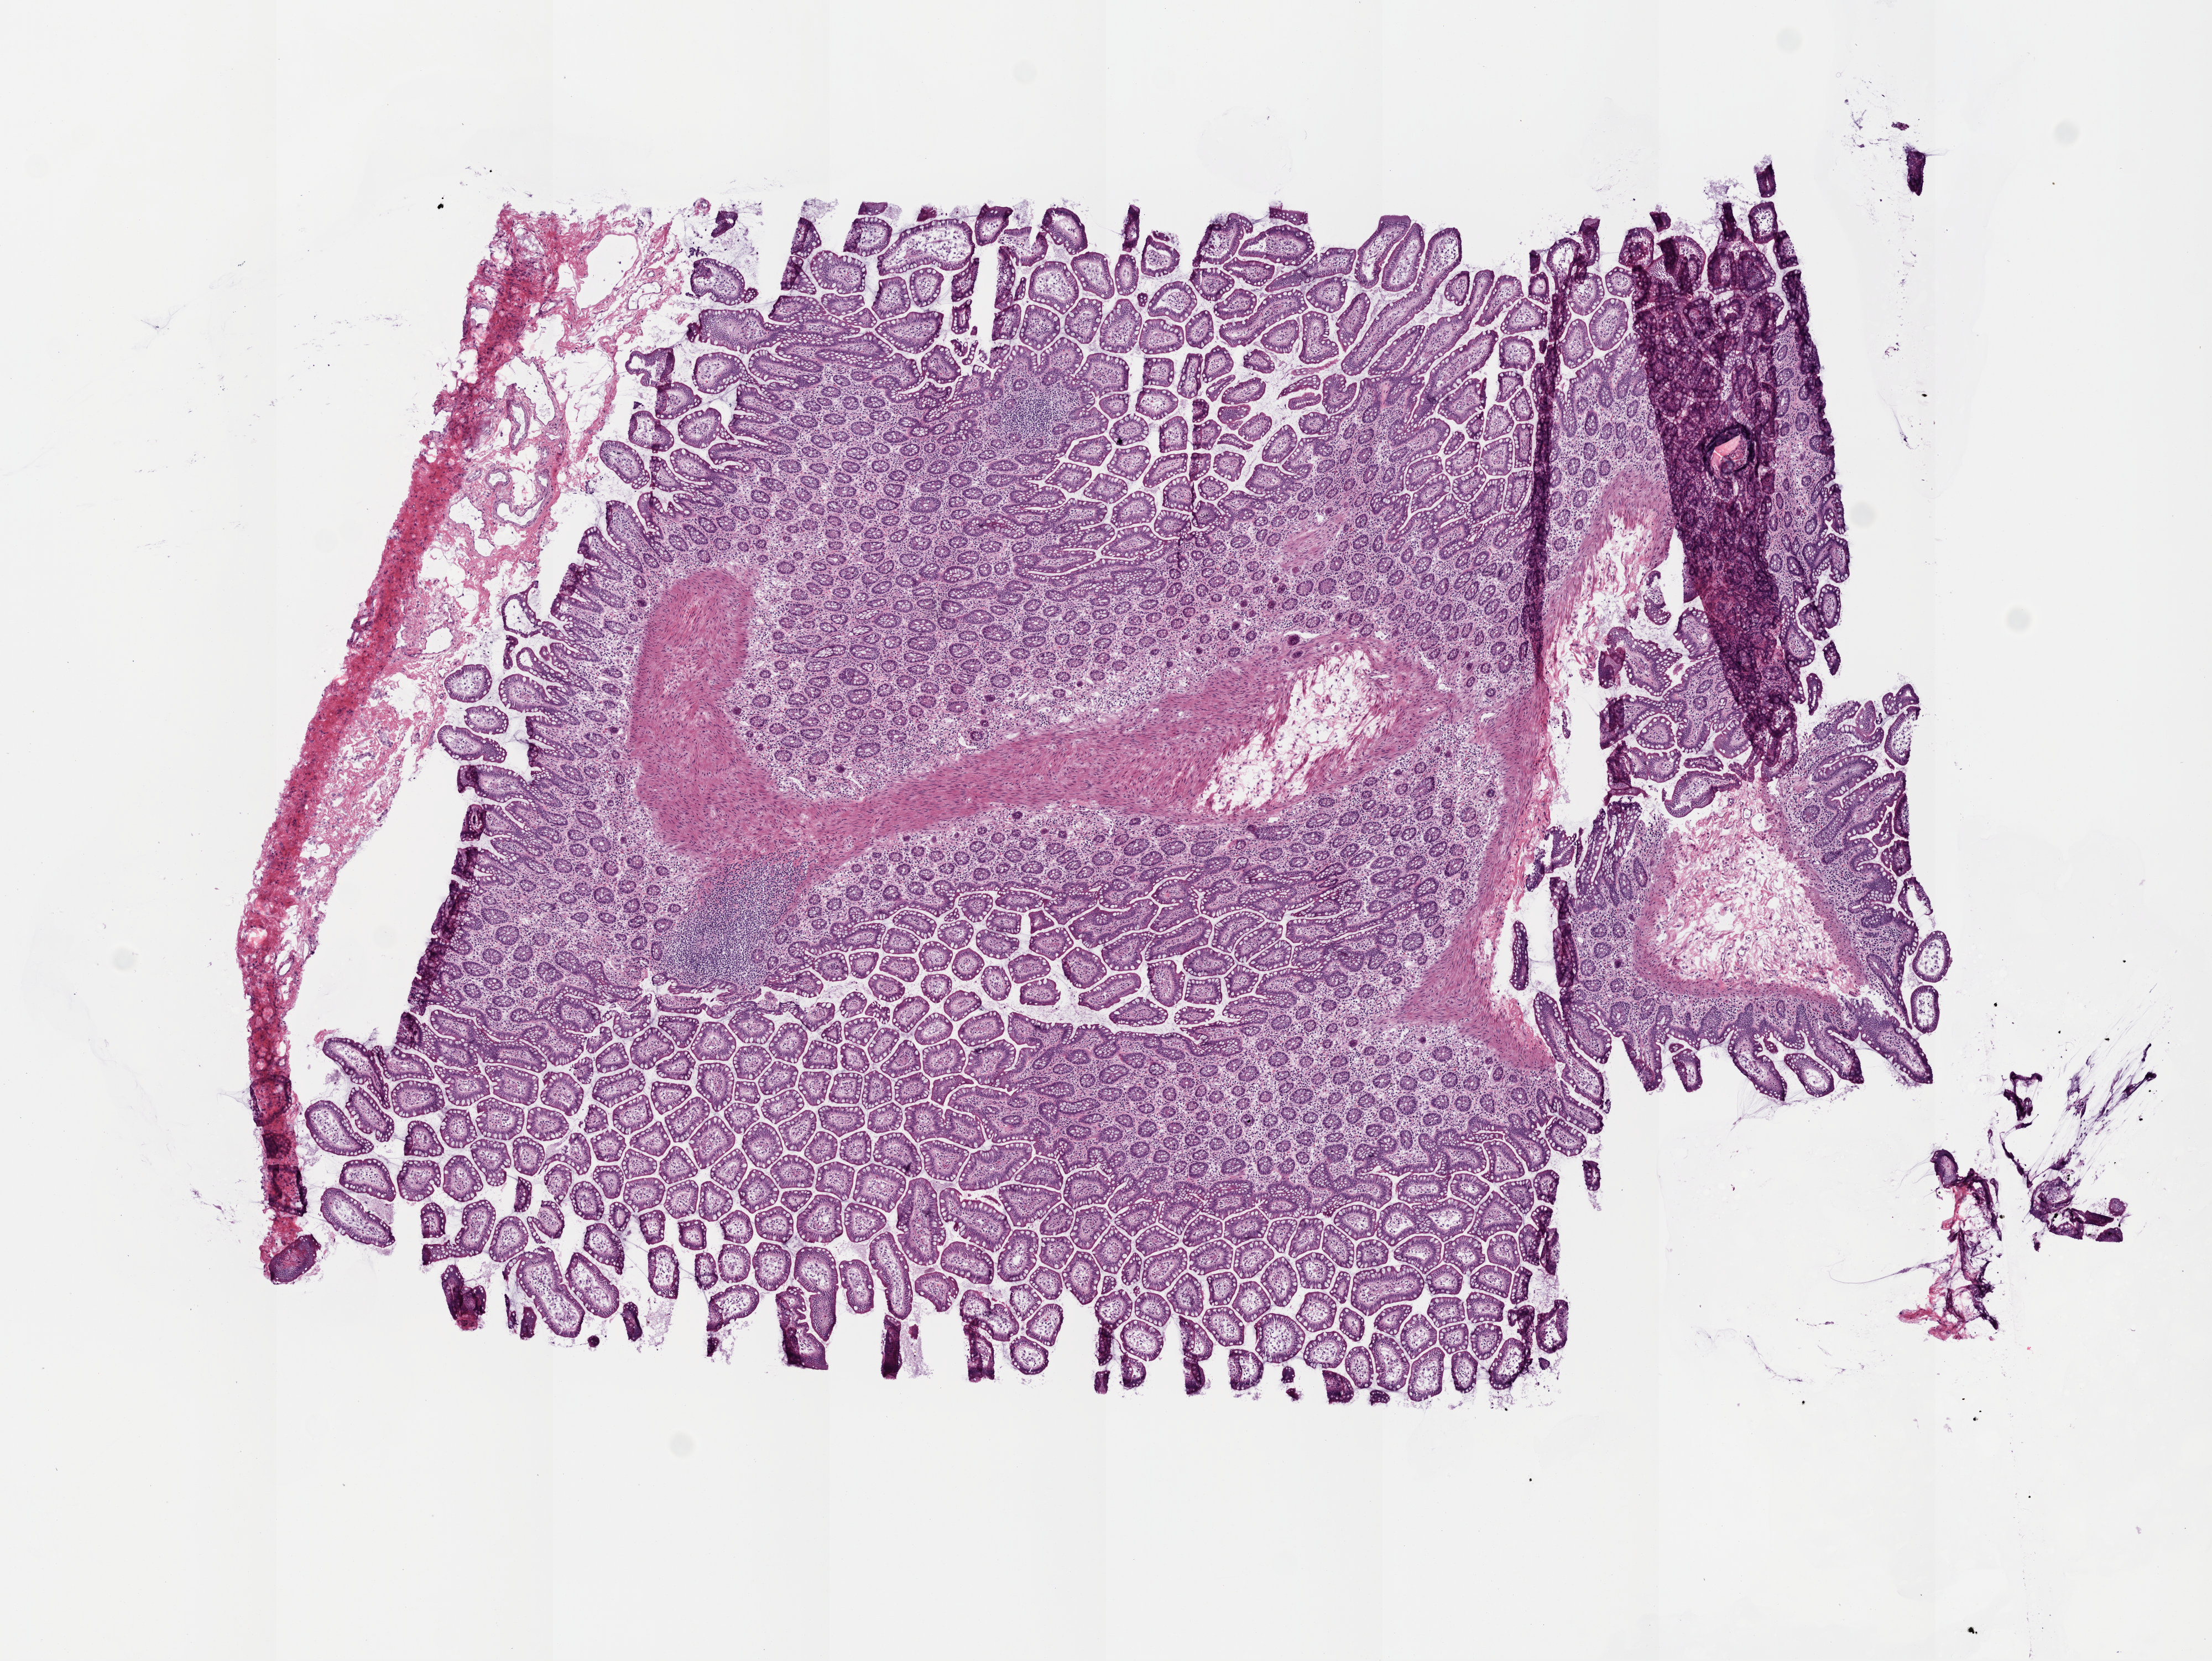
H&E whole-slide image, low-resolution overview of the scanned area, about 8.0 x 6.0 mm. Frozen section from the top of the tissue portion. Solid tissue normal (non-tumour tissue) sample from the colon. Female, age 72 years at initial diagnosis.
This section: solid tissue normal sample (biorepository sample class). Patient diagnosis: Adenocarcinoma, NOS (hepatic flexure of colon).